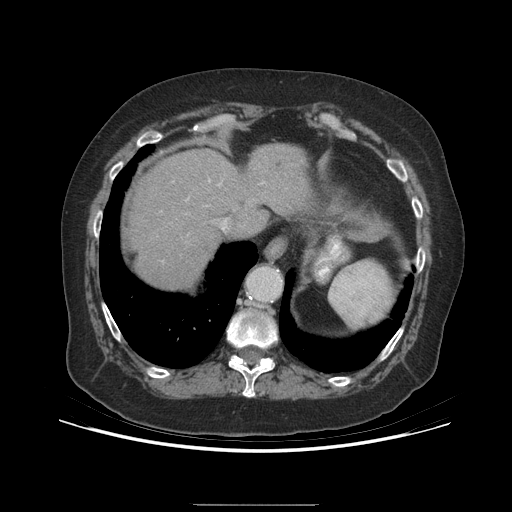
Contrast-enhanced abdominal CT (liver protocol), one axial slice; position 176 of 192 along the scan axis; 140 kVp; soft-tissue window (W 400 / L 40 HU); 512 × 512 image matrix, field of view 400 × 400 mm. From the clinical record (not read from this slice): diagnosis: hepatocellular carcinoma (patient treated with transarterial chemoembolisation; whether this scan precedes or follows treatment is not stated here); TNM stage (as recorded): Stage-I.
Structures marked on this image (semi-automatically segmented with operator editing):
- liver parenchyma outside the tumour (the mass and vessels are separate outlines, so this box may not span the whole liver): bounding box <130,144,310,288> (left, top, right, bottom; pixels)